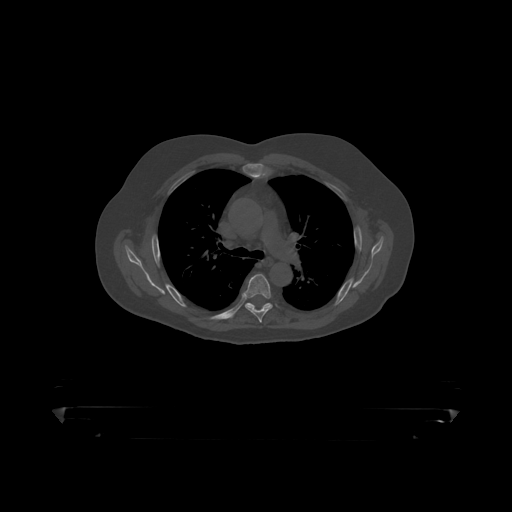
CT including the spine, one axial slice. Position 316 of 390 along the scan axis. Reconstruction kernel STANDARD. 120 kVp. Bone window (W 1800 / L 400 HU). 1.25 mm slice thickness. 512 × 512 image matrix, field of view 650 × 650 mm. Patient: male, 60 years. From the clinical record (not read from this slice): primary cancer: prostate.
Annotated regions visible in this slice (semi-automatic segmentation, software-assisted and operator-edited):
- T5 vertebra: bounding box <243,274,273,319> (left, top, right, bottom; pixels)
- T6 vertebra: <245,303,273,309>